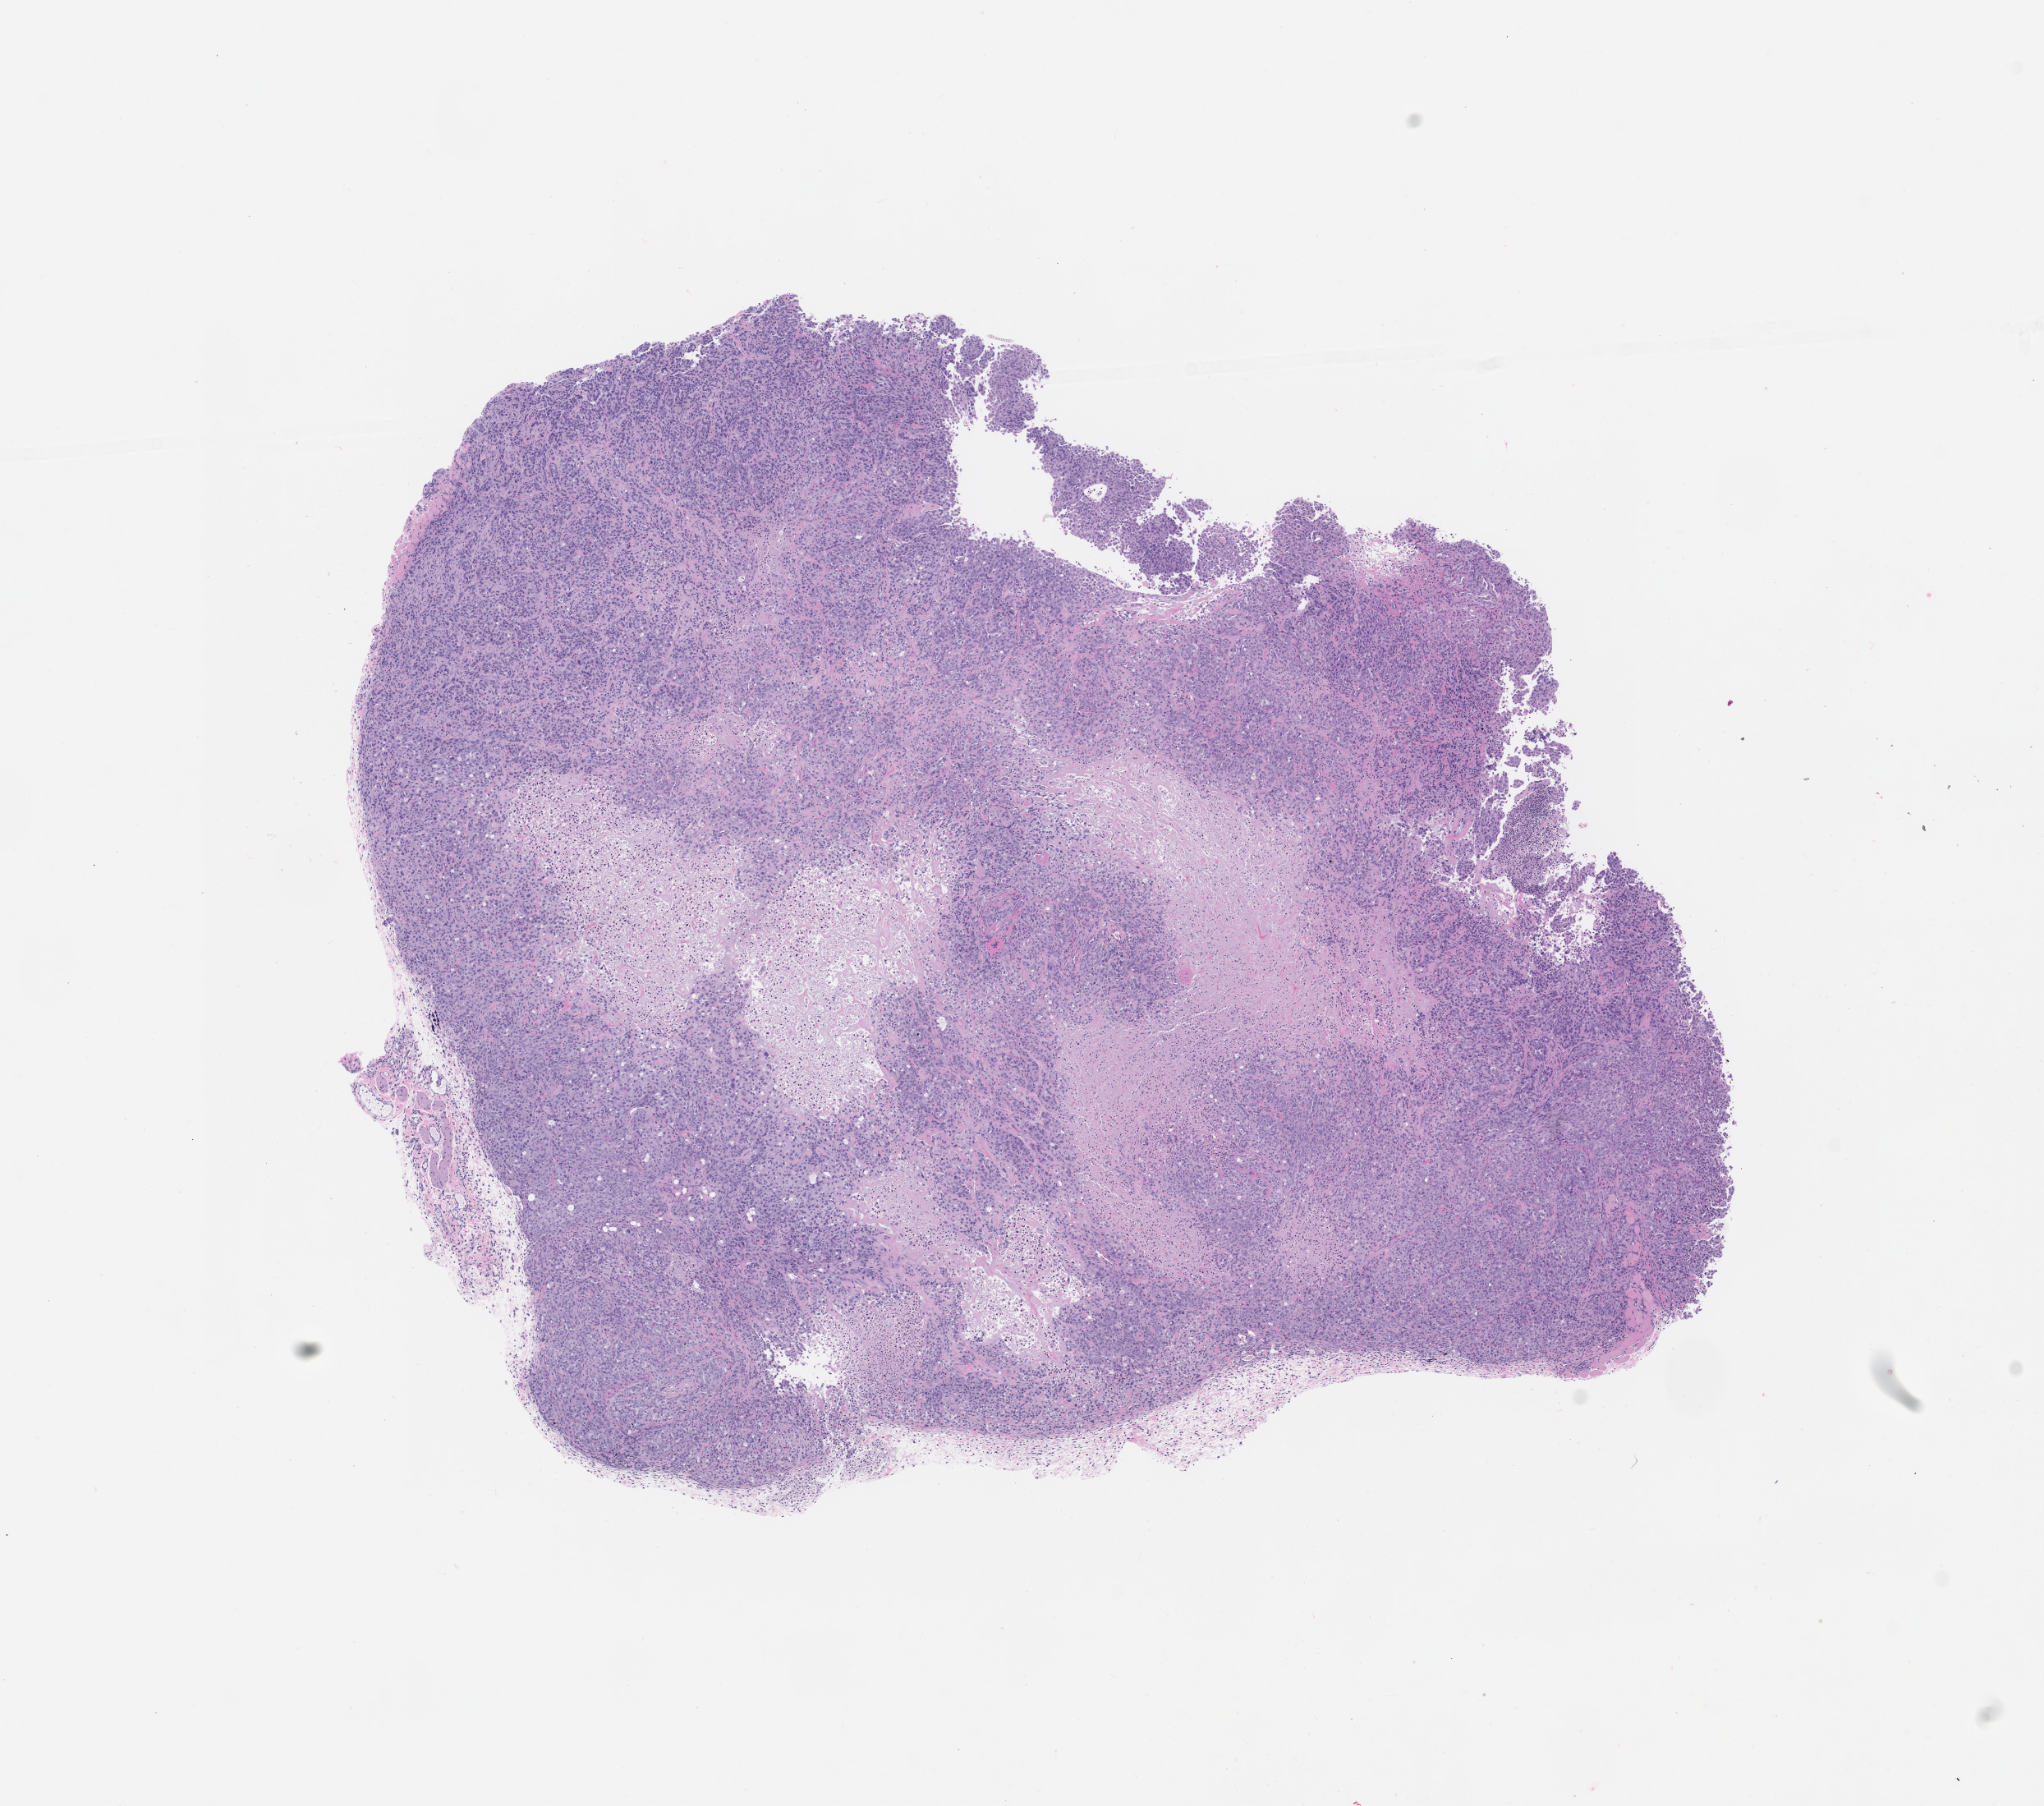
Whole-slide image, H&E: patient-derived xenograft (human tumor grown in a mouse), passage 0, a low-resolution overview of the entire scanned area, about 10.0 x 8.8 mm; FFPE section; originating tumor site category: lung.
Originating patient diagnosis: Lung Adenocarcinoma.